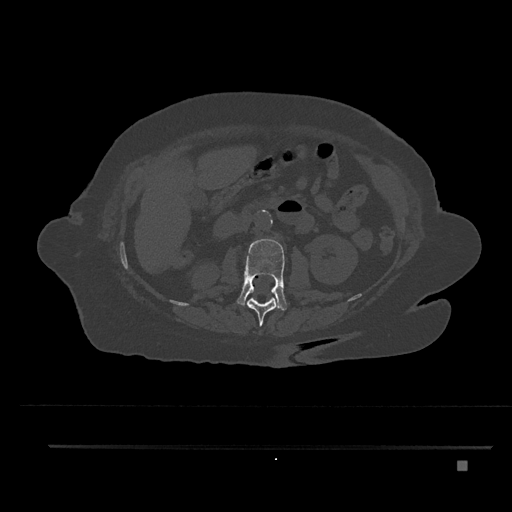
CT including the spine, one axial slice; reconstruction kernel Br40s/3; 120 kVp; bone window (W 1800 / L 400 HU); 0.5 mm slice thickness; 512 × 512 image matrix, field of view 437 × 437 mm. Female patient, age 76 years. Case-level facts recorded for this patient, not image findings: primary cancer: lung.
Outlined on this slice (semi-automatically segmented with operator editing):
- L1 vertebra: bounding box (x1, y1, x2, y2) in pixels: (247, 298, 279, 326)
- L2 vertebra: (237, 238, 287, 311)